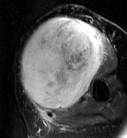
MRI of an extremity soft-tissue mass, one axial slice. Position 41 of 87 along the scan axis. T2-weighted fat-saturated. MR volume resampled by the dataset authors to the PET/CT grid (not the native acquisition matrix). 3.27 mm slice thickness. 127 × 138 image matrix, field of view 124 × 135 mm. Female patient. From the clinical record (not read from this slice): histological type: pleiomorphic leiomyosarcoma; grade: high; site of the primary tumour: left biceps.
Outlined on this slice (expert contour drawn on MRI and transferred to this co-registered scan by the dataset authors):
- gross tumour volume including surrounding oedema: bounding box [x1, y1, x2, y2] px = [20, 18, 108, 113]
- gross tumour volume (mass): [20, 18, 105, 111]